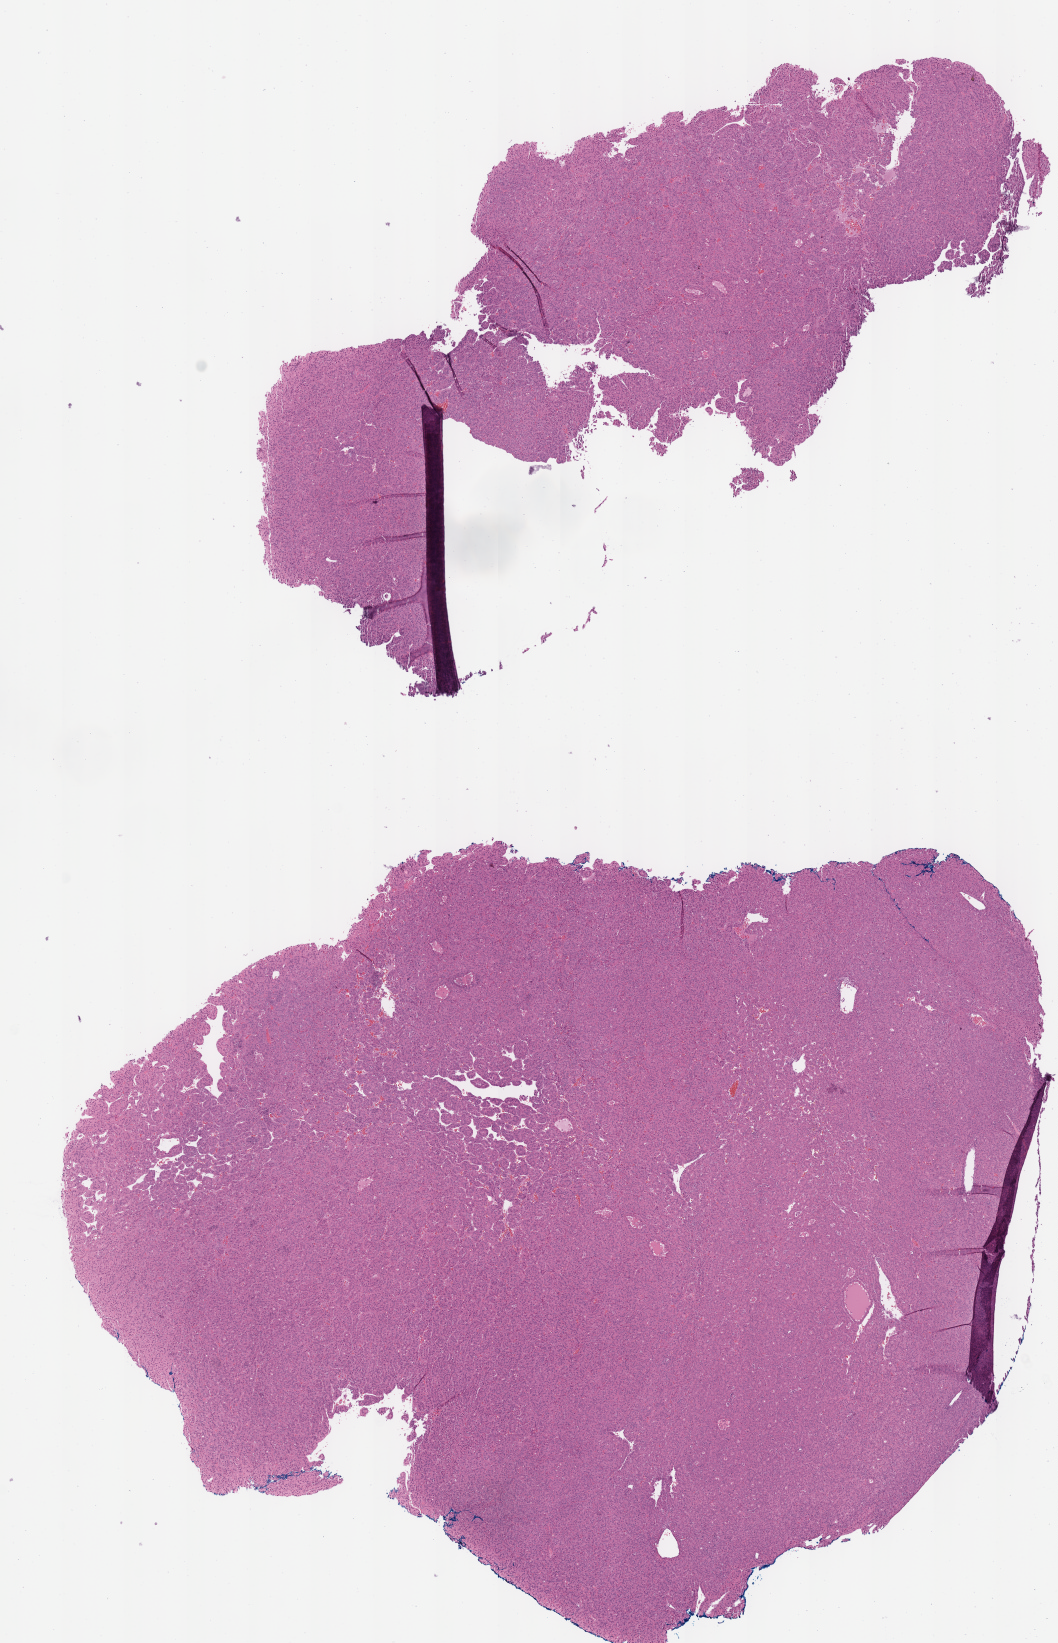
Digitized H&E tissue section (whole slide) — a low-resolution overview of the entire scanned area, about 8.3 x 12.9 mm. FFPE section. Liver, primary tumour sample. Patient: male, age at initial diagnosis 75 years.
• AJCC pathologic stage: I
• histologic diagnosis: Hepatocellular carcinoma, NOS